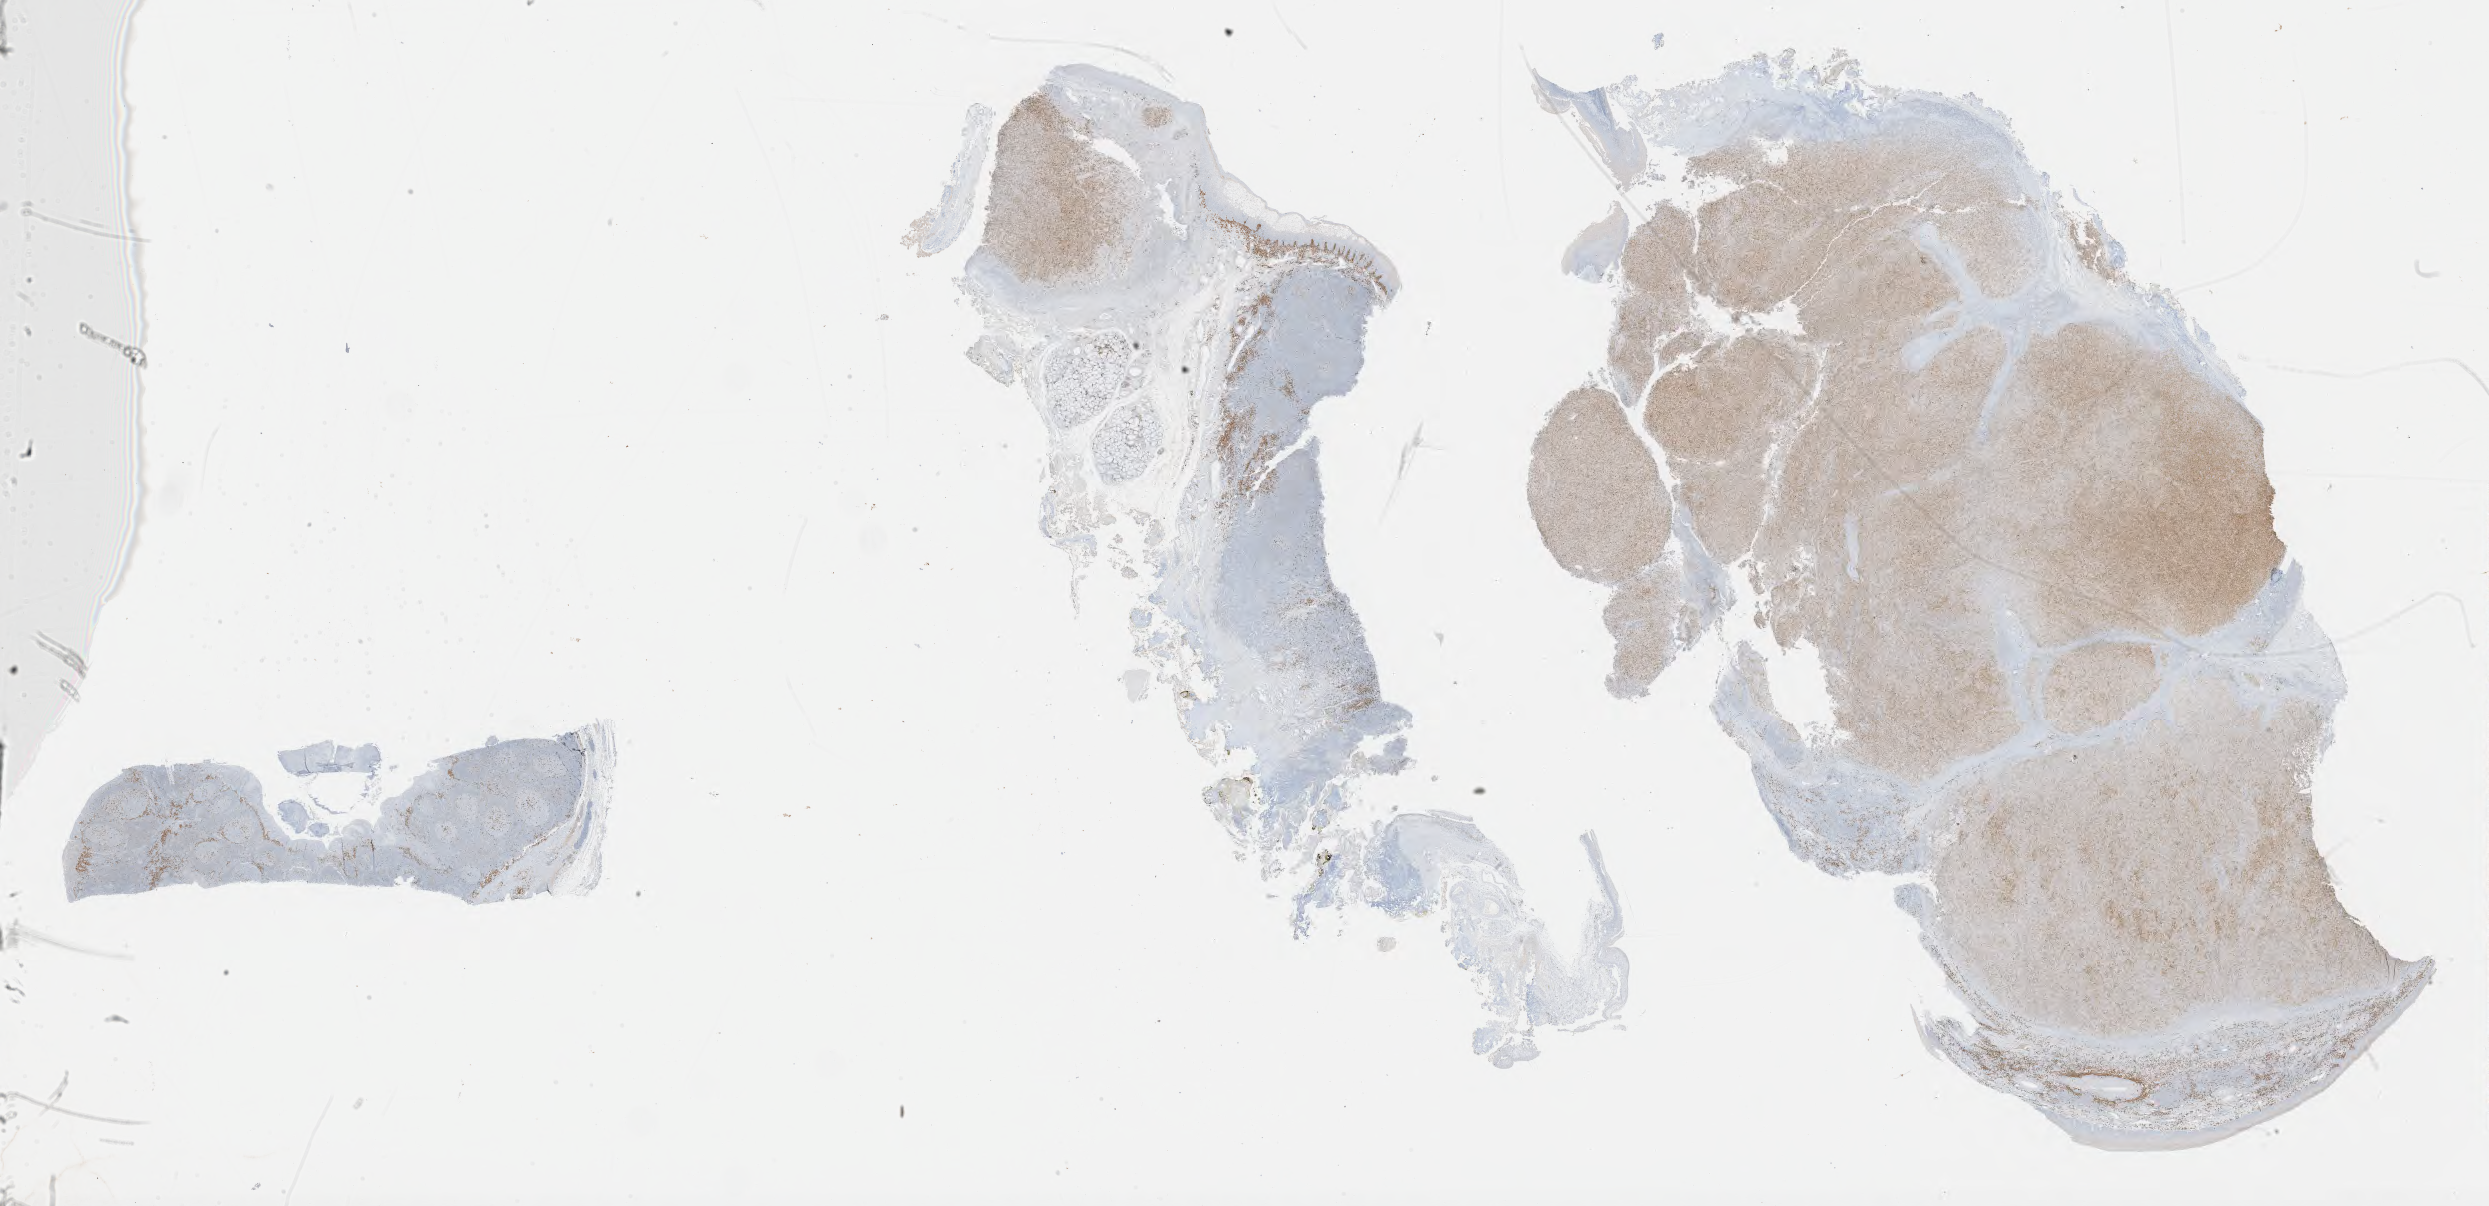
IHC for IRF4/MUM1, whole-slide image — whole scanned area (about 40.3 x 19.5 mm) shown as a low-resolution overview; tumor tissue; site: lymph node. Patient male; aged 56.
Diagnosis: Diffuse large B-cell lymphoma, NOS.